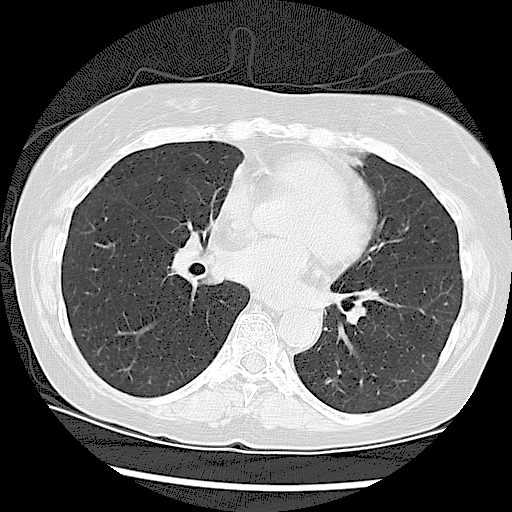
Low-dose screening chest CT, one axial slice. Position 48 of 108 along the scan axis. Reconstruction kernel LUNG. 120 kVp. Lung window (W 1500 / L -600 HU). 2.5 mm slice thickness. 512 × 512 image matrix, field of view 330 × 330 mm.
Outlined on this slice (outlined manually by an expert reader):
- lesion 1 (tumor, lower lobe of left lung): bounding box [x1, y1, x2, y2] px = [325, 378, 335, 386]